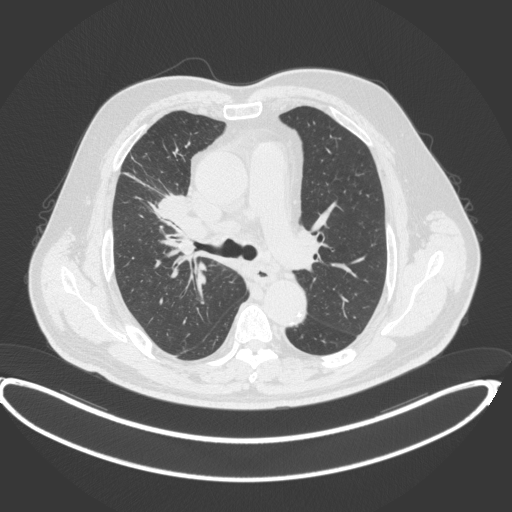
Chest CT, one axial slice. Position 265 of 395 along the scan axis. 120 kVp. Lung window (W 1500 / L -600 HU). 1 mm slice thickness. 512 × 512 image matrix, field of view 448 × 448 mm. Patient: male, 62 years. From the clinical record (not read from this slice): clinical TNM (as recorded): T1c N3 M1c.
Outlined on this slice (rectangle marked by the reading radiologist):
- lung tumour (recorded histology: adenocarcinoma): box from (x=146, y=191) to (x=192, y=222) px